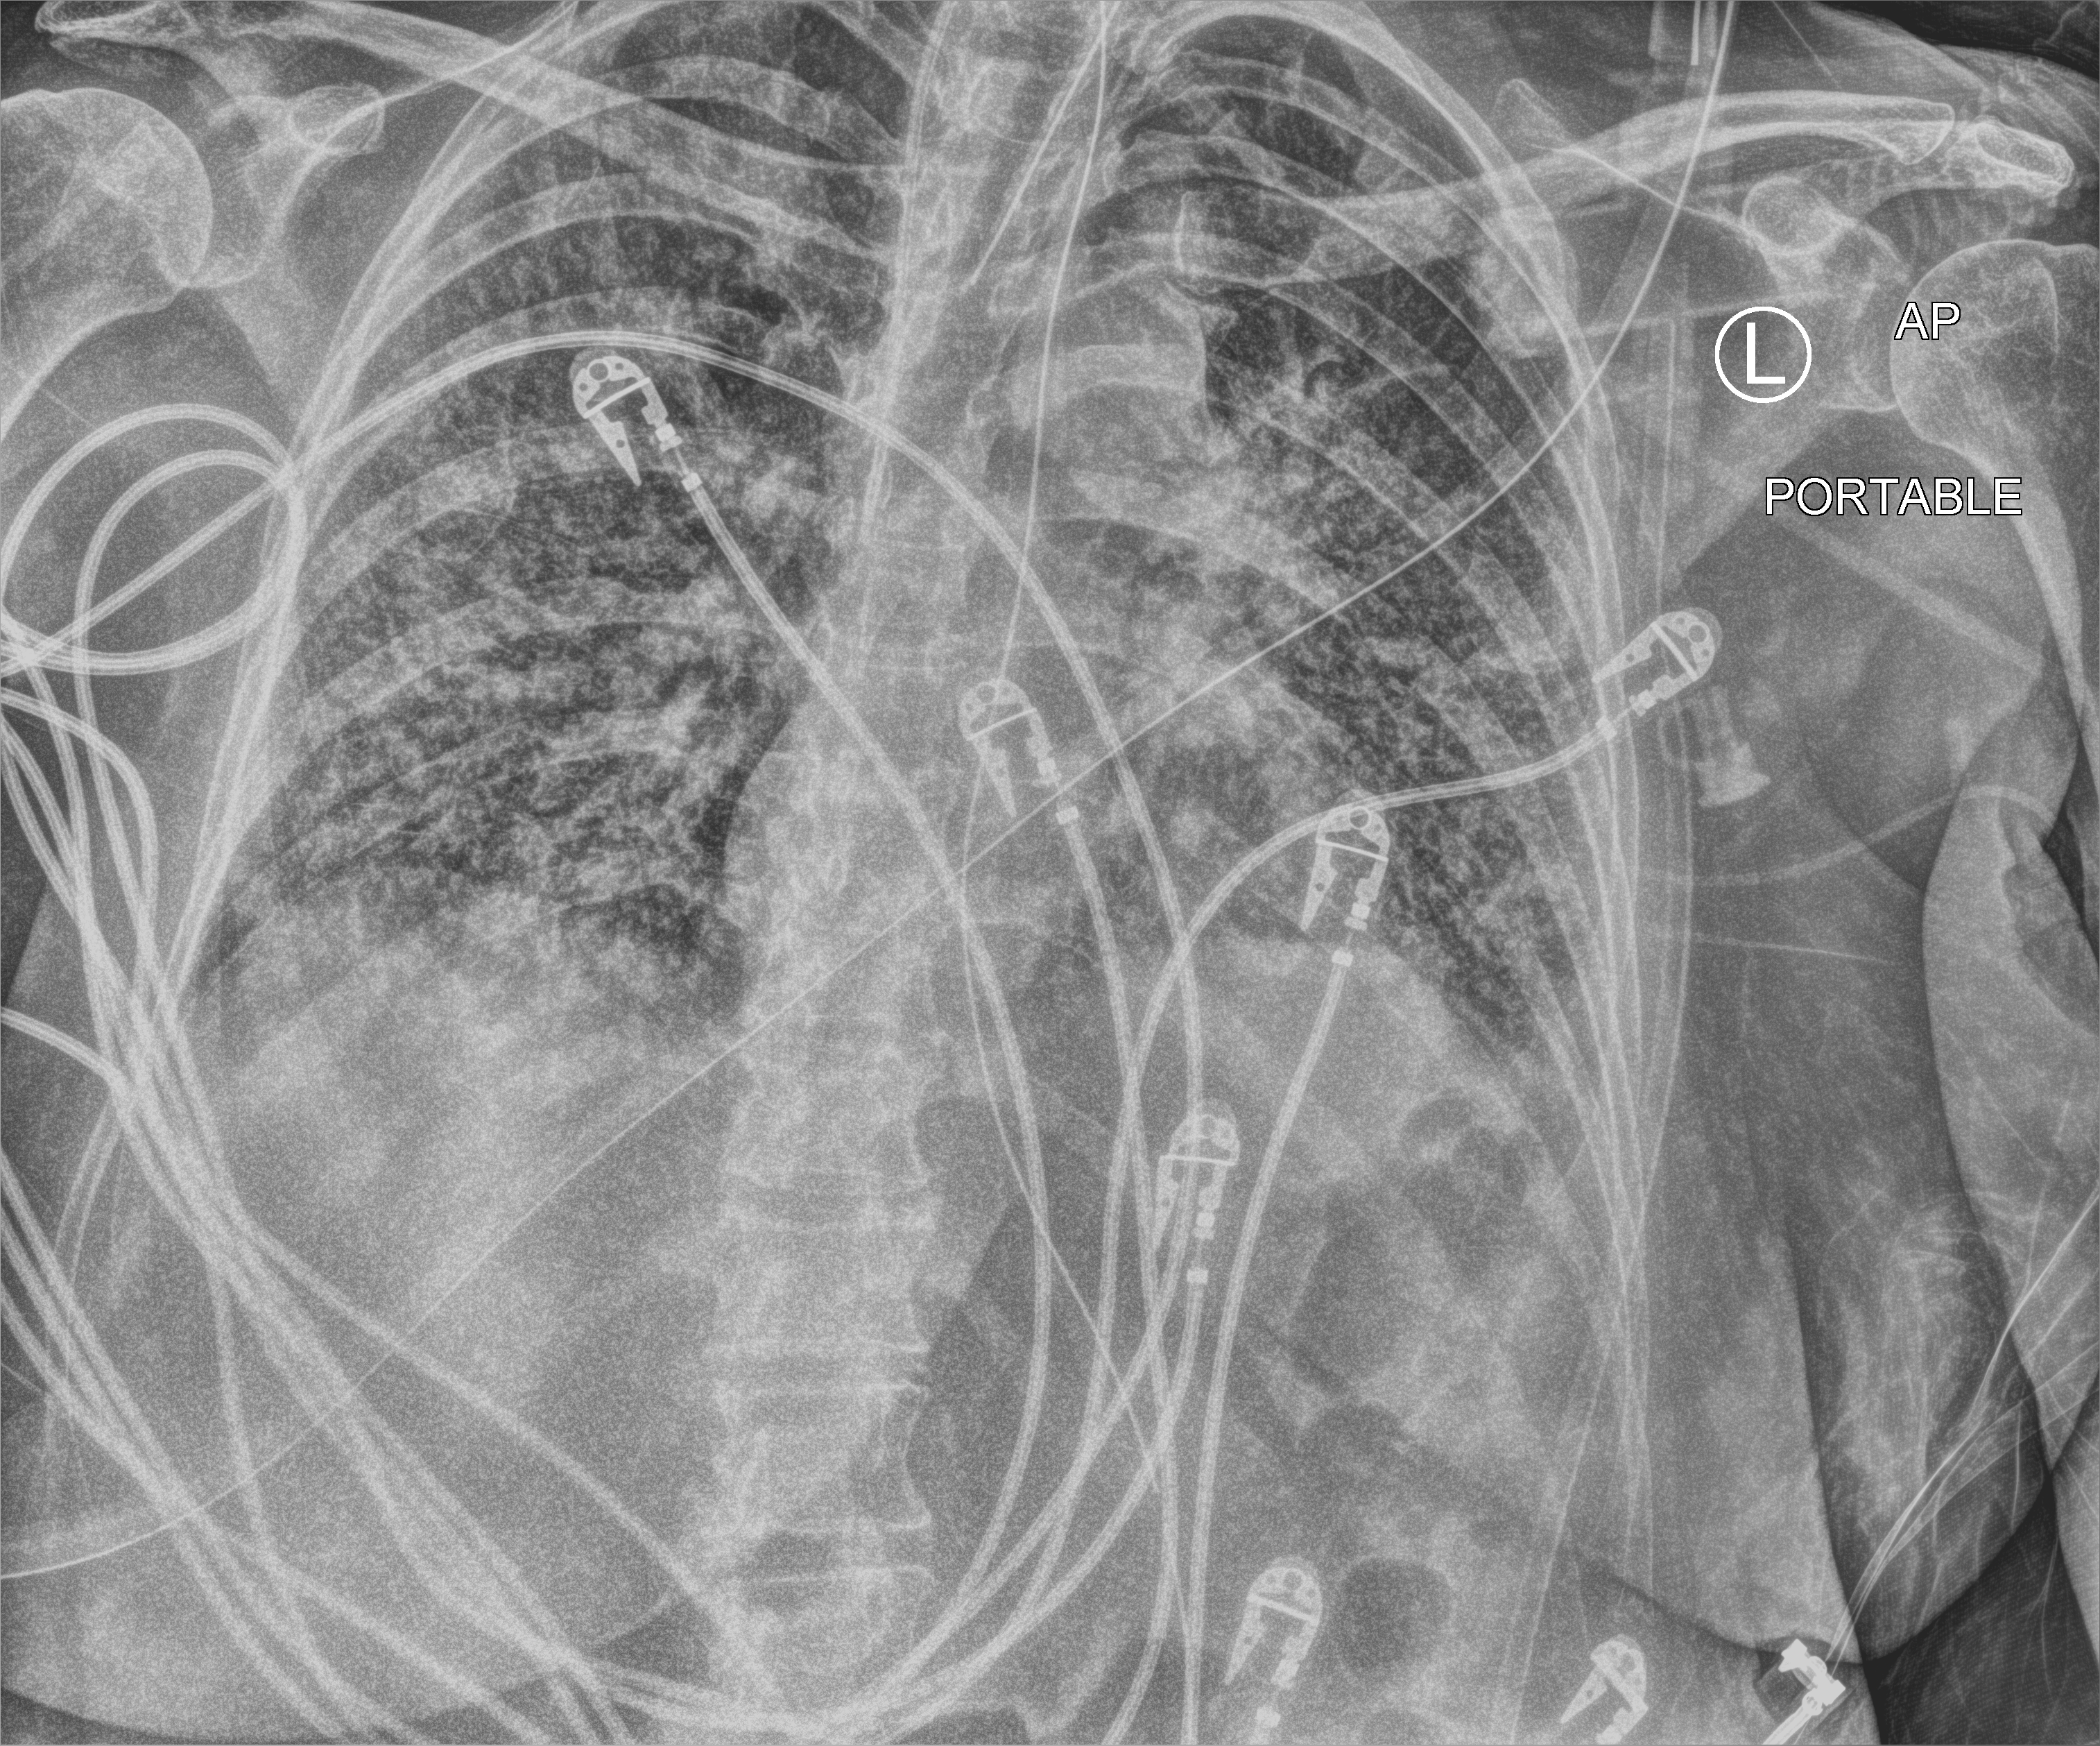
Chest X-ray (portable); anteroposterior (AP) projection. Patient hospitalised with COVID-19; female, aged 60–74 years.
Admission-level facts for this patient (not findings on this image; timing relative to this image not recorded): admitted to intensive care during this hospital stay: yes.